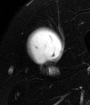
MRI of an extremity soft-tissue mass, one axial slice; position 44 of 65 along the scan axis; T2-weighted fat-saturated; MR volume resampled by the dataset authors to the PET/CT grid (not the native acquisition matrix); 90 × 105 image matrix. Male patient. From the clinical record (not read from this slice): histological type: mixoid liposarcoma; grade: low; site of the primary tumour: left thigh.
Annotated regions visible in this slice (expert contour drawn on MRI and transferred to this co-registered scan by the dataset authors):
- gross tumour volume (mass): bounding box (x1, y1, x2, y2) in pixels: (27, 31, 60, 65)